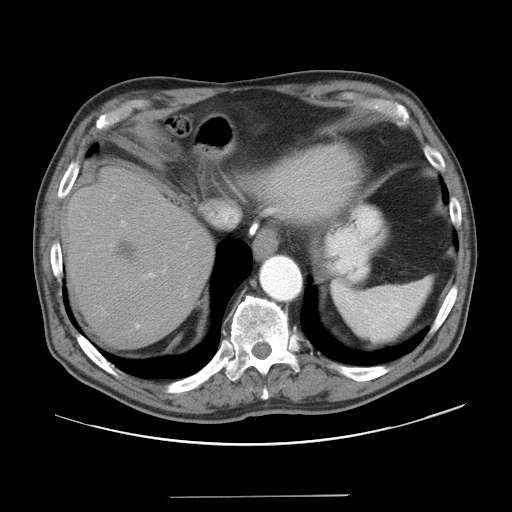
Contrast-enhanced abdominal CT, one axial slice. Position 34 of 41 along the scan axis. Reconstruction kernel STANDARD. Soft-tissue window (W 400 / L 40 HU). 5 mm slice thickness. 512 × 512 image matrix, field of view 420 × 420 mm. Male patient, age 75 years. From the clinical record (not read from this slice): diagnosis: colorectal cancer liver metastases, imaged before liver resection; multiple liver metastases: no; largest metastasis: 5.2 cm; disease in both lobes: no.
Structures marked on this image (expert manual segmentation):
- hepatic veins: bounding box [x1, y1, x2, y2] px = [210, 207, 237, 224]
- liver: [70, 170, 211, 346]
- planned liver remnant (the part of the liver to remain after resection): [93, 217, 211, 346]
- portal vein (with intrahepatic branches): [121, 220, 155, 329]
- liver metastasis: [116, 241, 137, 259]